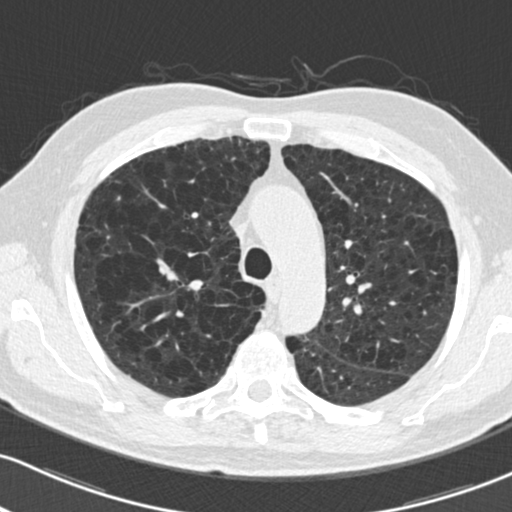
Low-dose screening chest CT, axial slice, second screening round (one year after baseline), lung window (W 1500 / L -600 HU), 512 × 512 image matrix. Male participant, aged 73 years at enrolment.
Expert reader's lesion annotation, box from (x=148, y=258) to (x=198, y=292) px. The exam's reader record, not a measurement of the box and not confirmed to be the same lesion: non-calcified nodule or mass ≥4 mm, right upper lobe, 10 × 9 mm, smooth margins, soft tissue attenuation, pre-existing on the prior screen: yes; interval growth: yes. Official screen result: positive, other. Participant outcome: lung cancer diagnosed 51 days after this screen — squamous cell carcinoma, NOS, right upper lobe, stage IA (AJCC 6th edition), 10 mm at pathology.